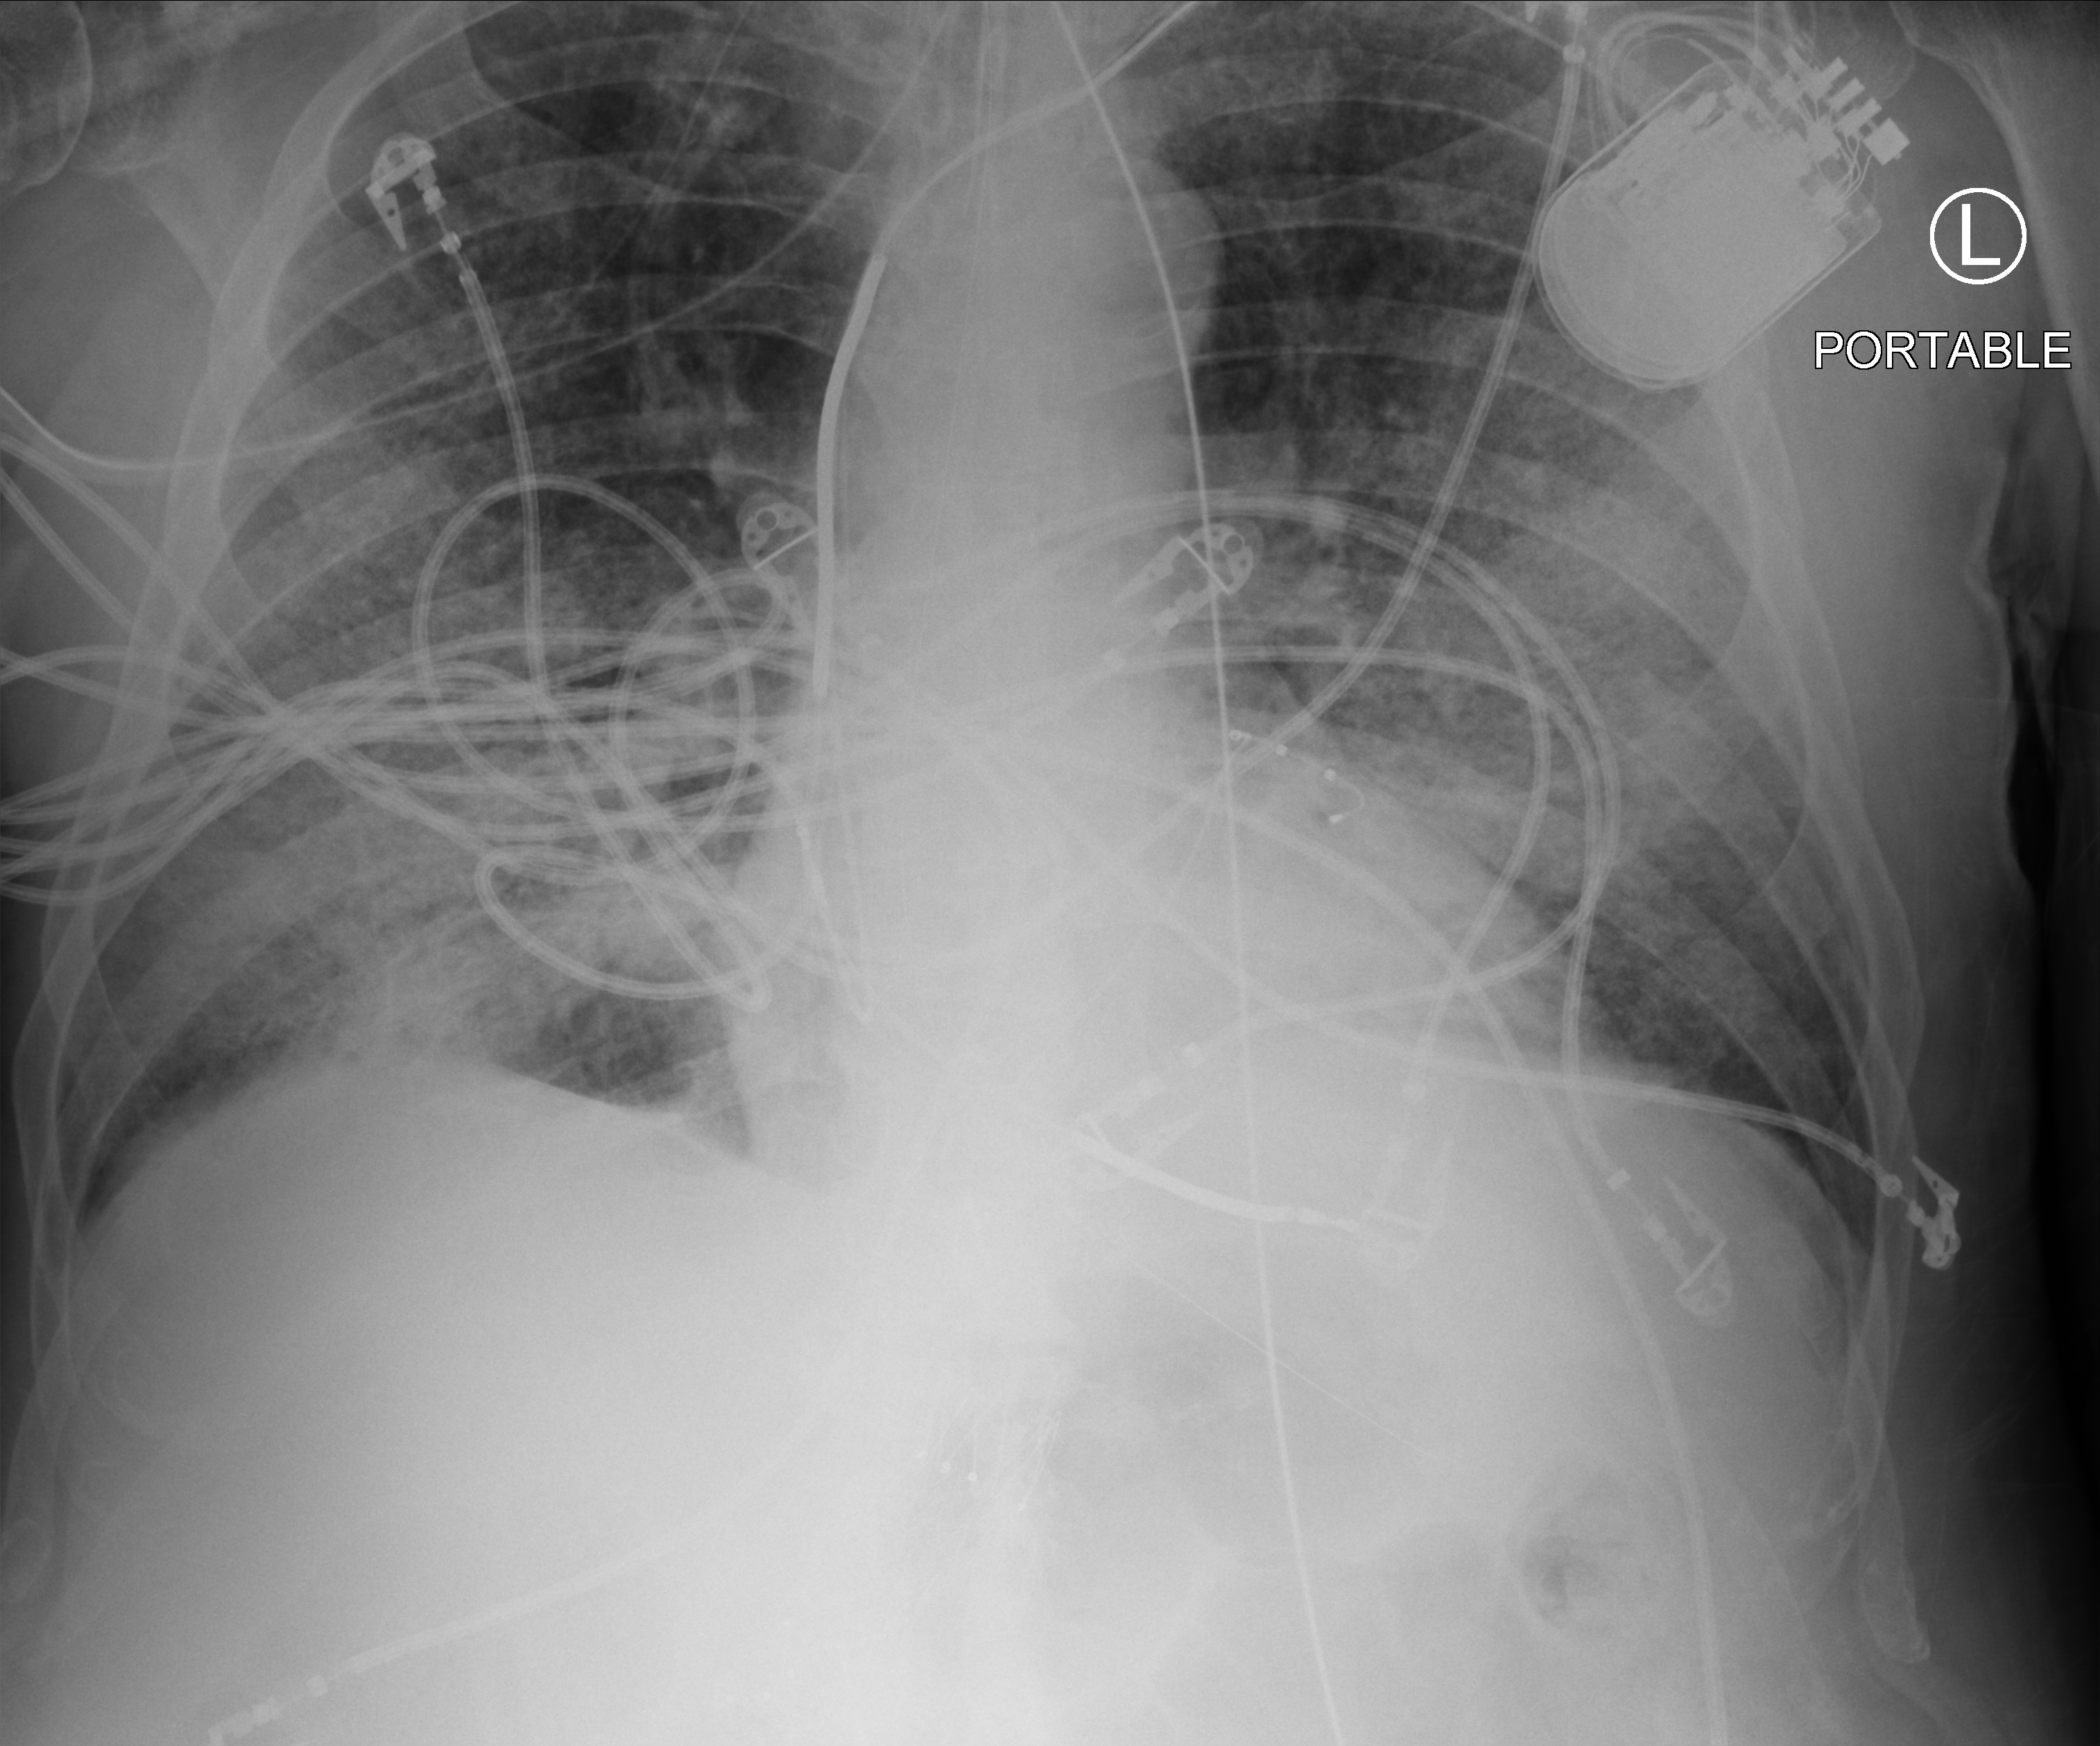
Bedside chest radiograph (computed radiography), anteroposterior (AP) projection. Patient hospitalised with COVID-19; male, aged 60–74 years.
Hospital-stay facts (about this admission, not read from this image; timing relative to this image not recorded): admitted to intensive care during this hospital stay: yes; length of hospital stay: 36 days; chronic kidney disease (admission record): no.